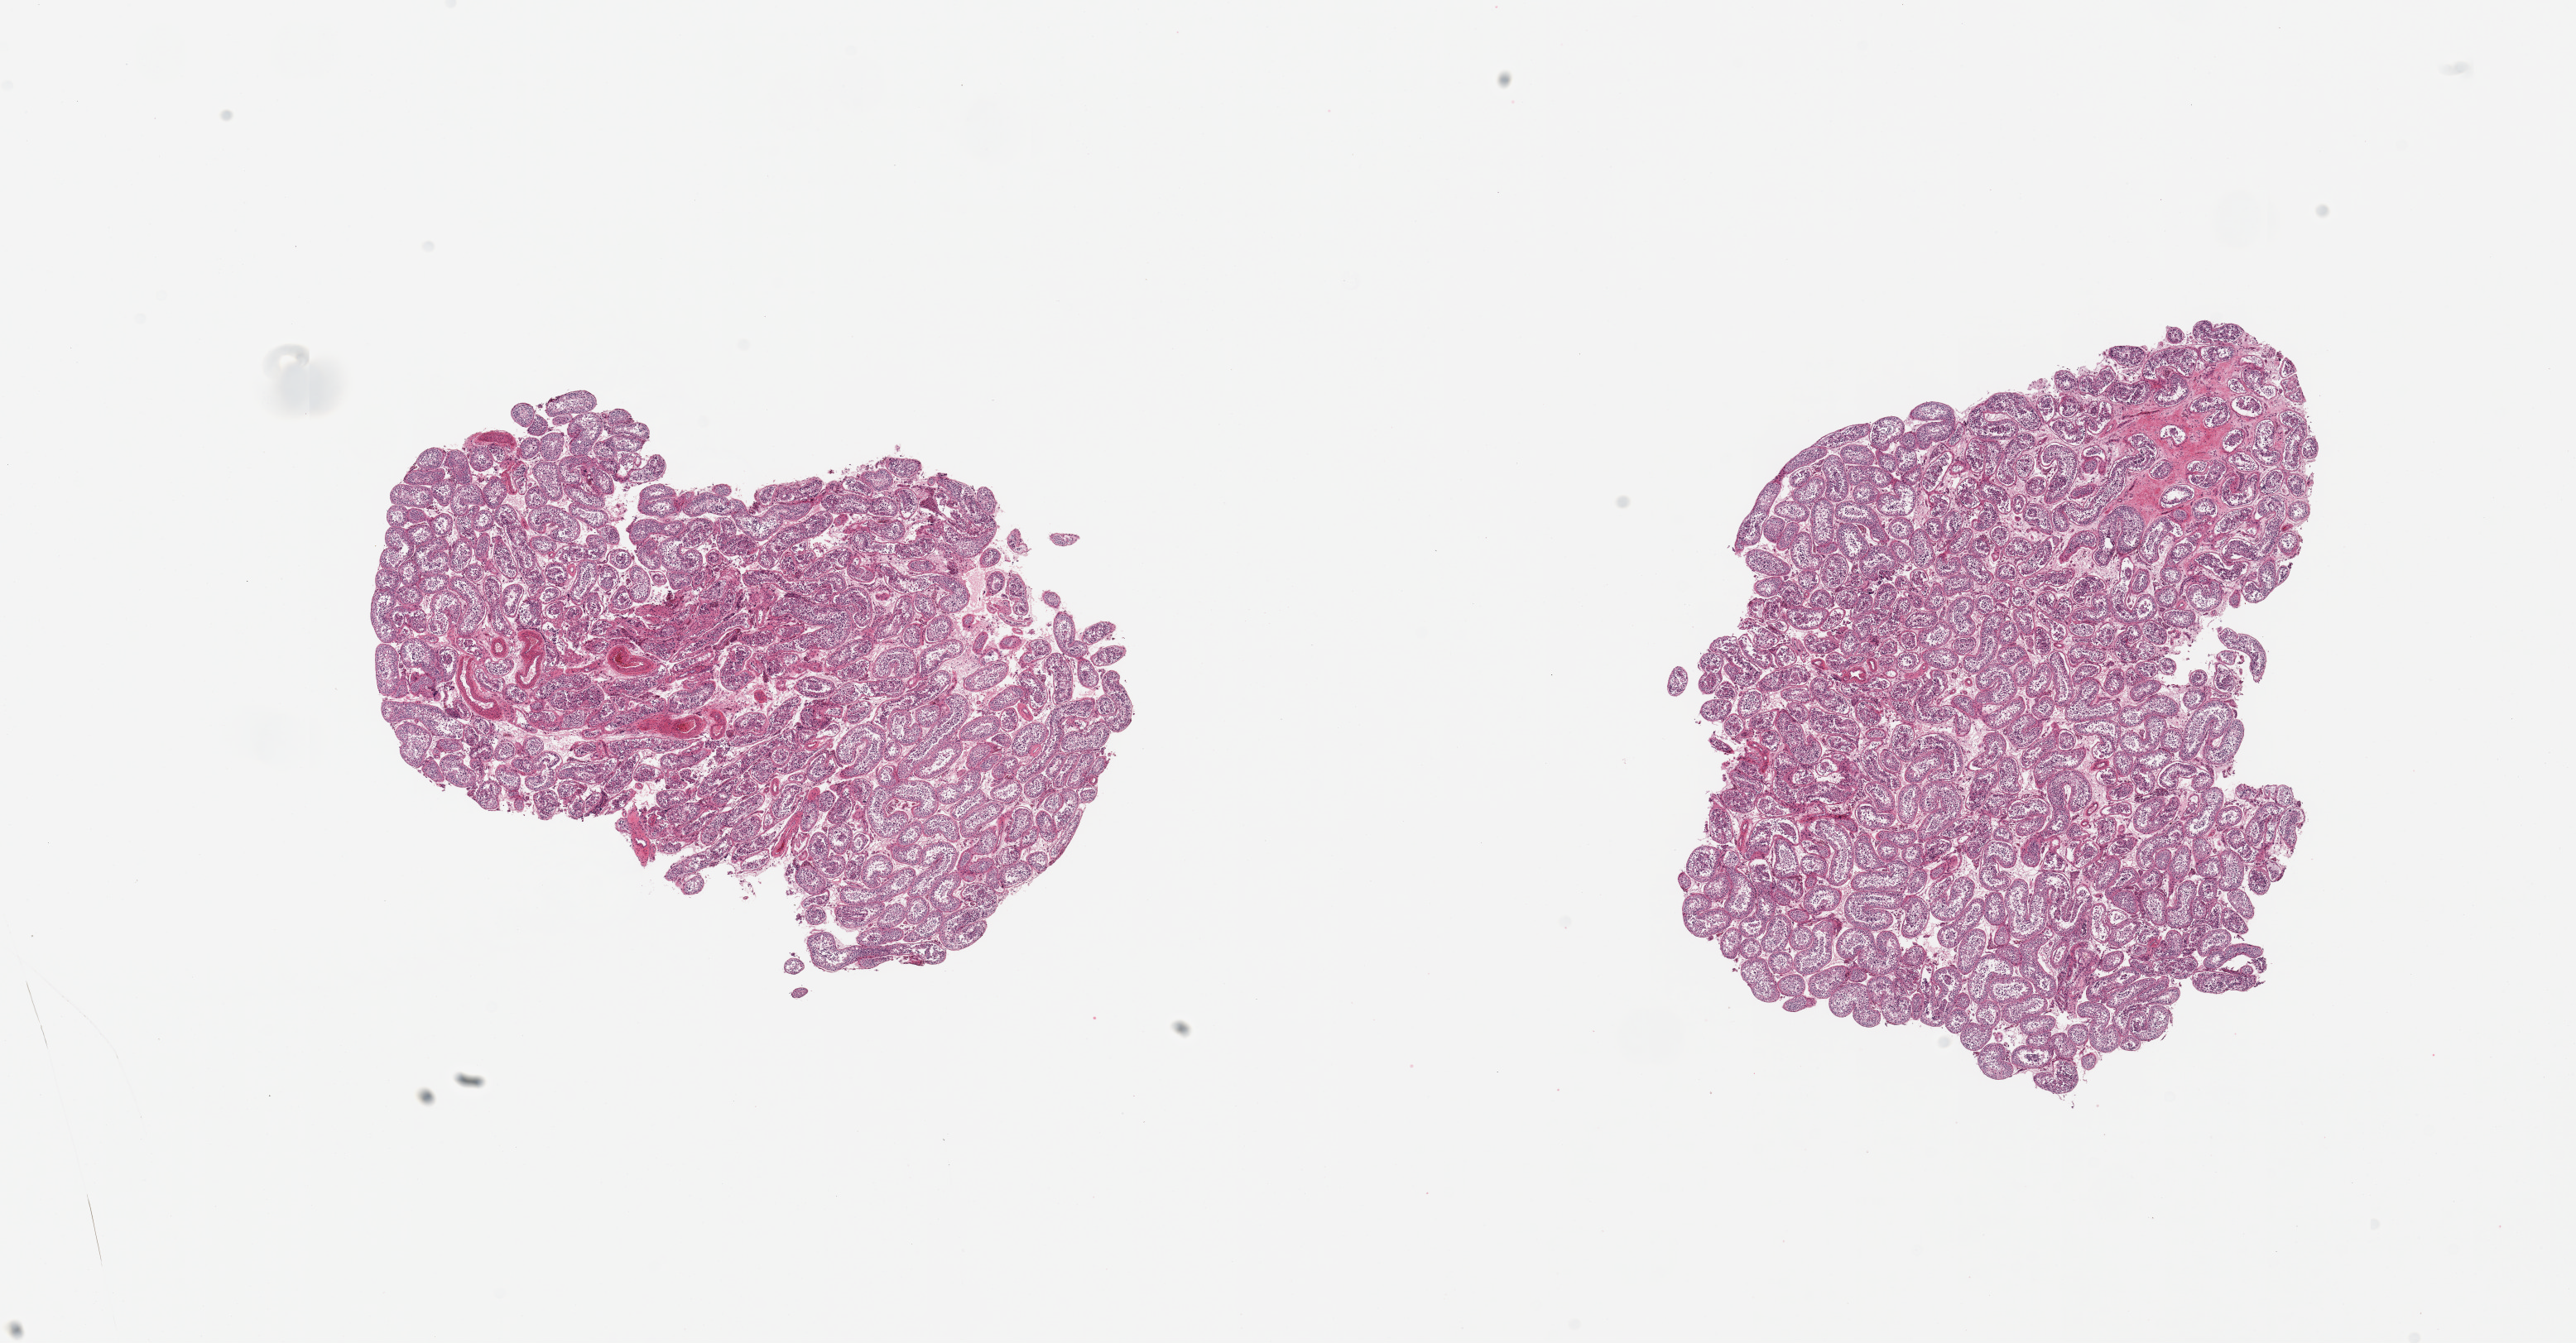
Whole-slide image, haematoxylin and eosin stain, low-resolution overview of the scanned area, about 24.6 x 12.8 mm, PAXgene-fixed paraffin-embedded (PFPE) section, sampled site (target tissue): testis, tissue donor sample.
* pathologist's review note for this sample: 2 pieces spermatogenesis present